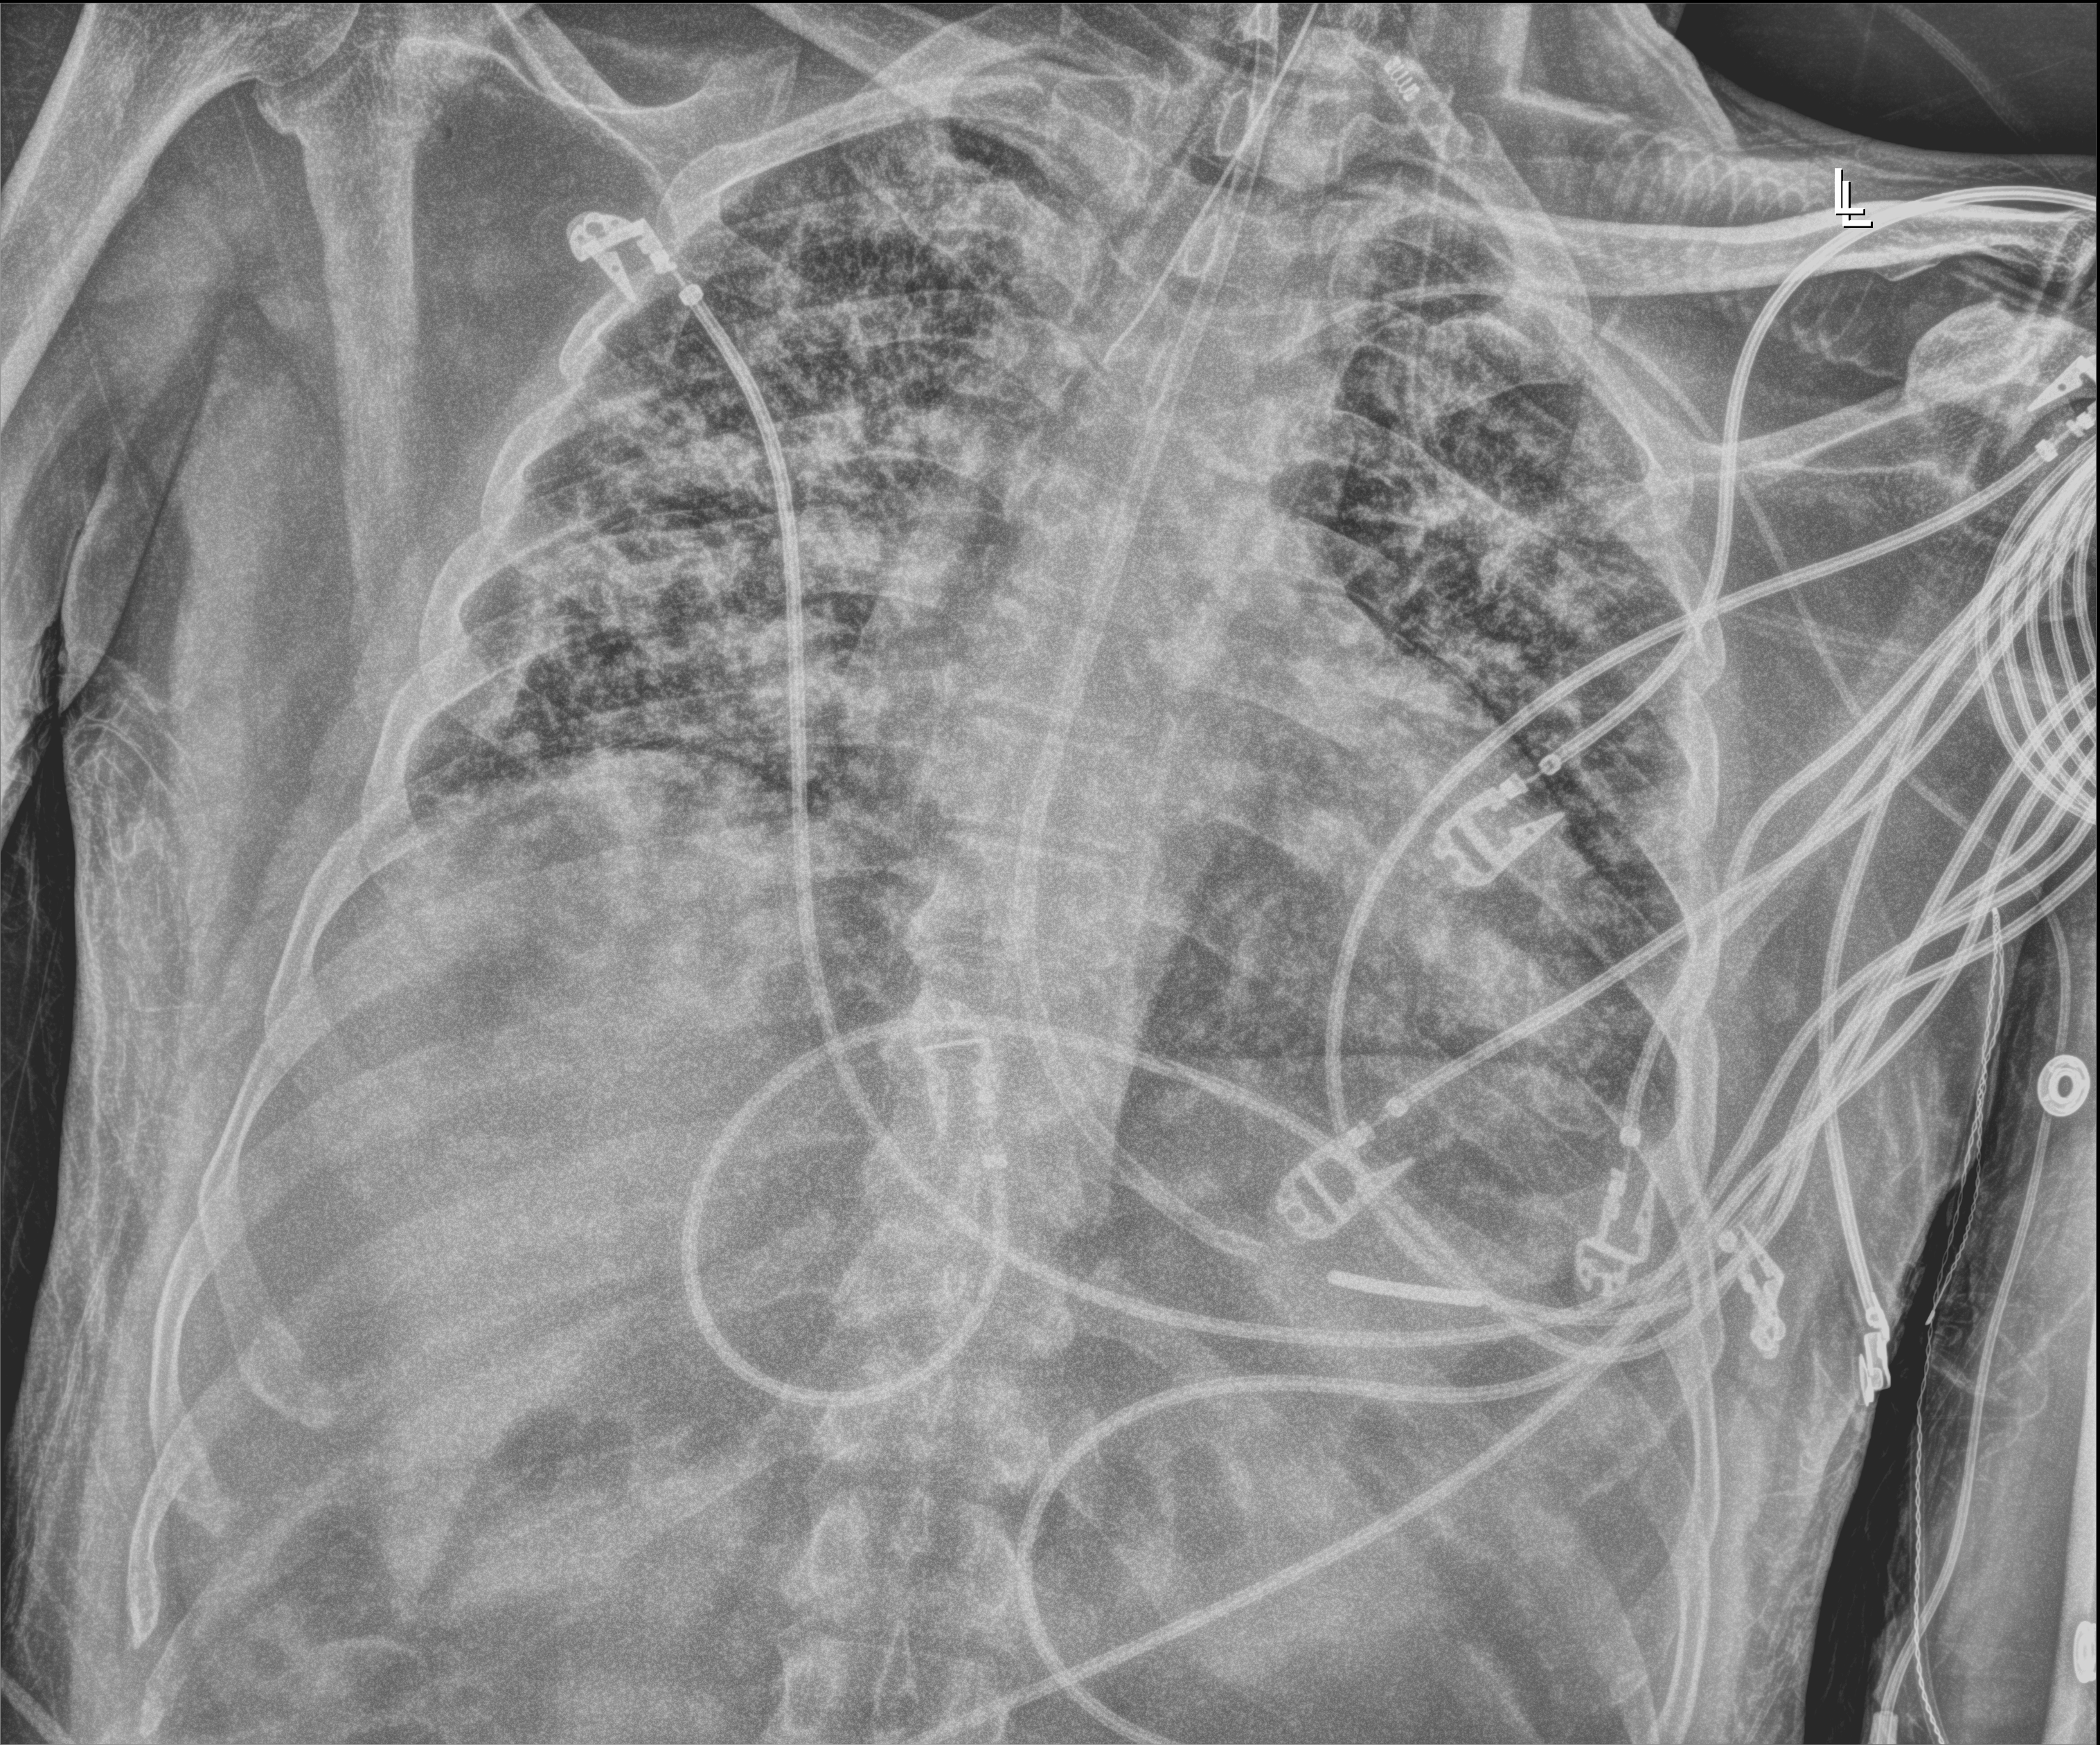
Bedside chest radiograph (digital radiography), anteroposterior (AP) projection. Male patient hospitalised with COVID-19, age 18–59 years.
Admission-level facts for this patient (not findings on this image; timing relative to this image not recorded):
- mechanically ventilated during this hospital stay: yes
- chronic kidney disease (admission record): no
- admitted to intensive care during this hospital stay: yes